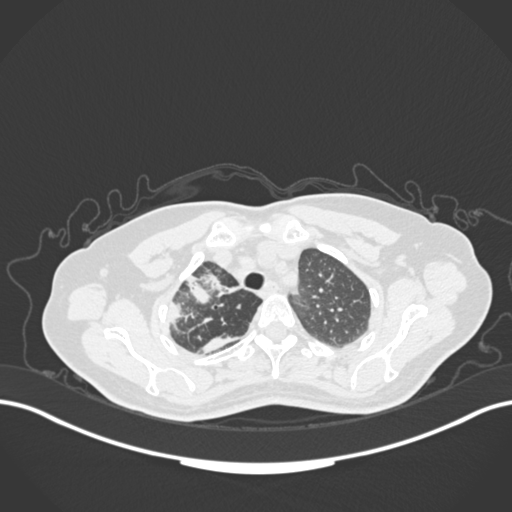
Chest CT, one axial slice; position 134 of 177 along the scan axis; reconstruction kernel B30f; 120 kVp; lung window (W 1500 / L -600 HU); 512 × 512 image matrix. Female patient, age 60 years. From the clinical record (not read from this slice): clinical TNM (as recorded): T3 N1 M1.
Outlined on this slice (bounding box drawn by a radiologist):
- lung tumour (recorded histology: adenocarcinoma): bounding box <165,270,240,327> (left, top, right, bottom; pixels)